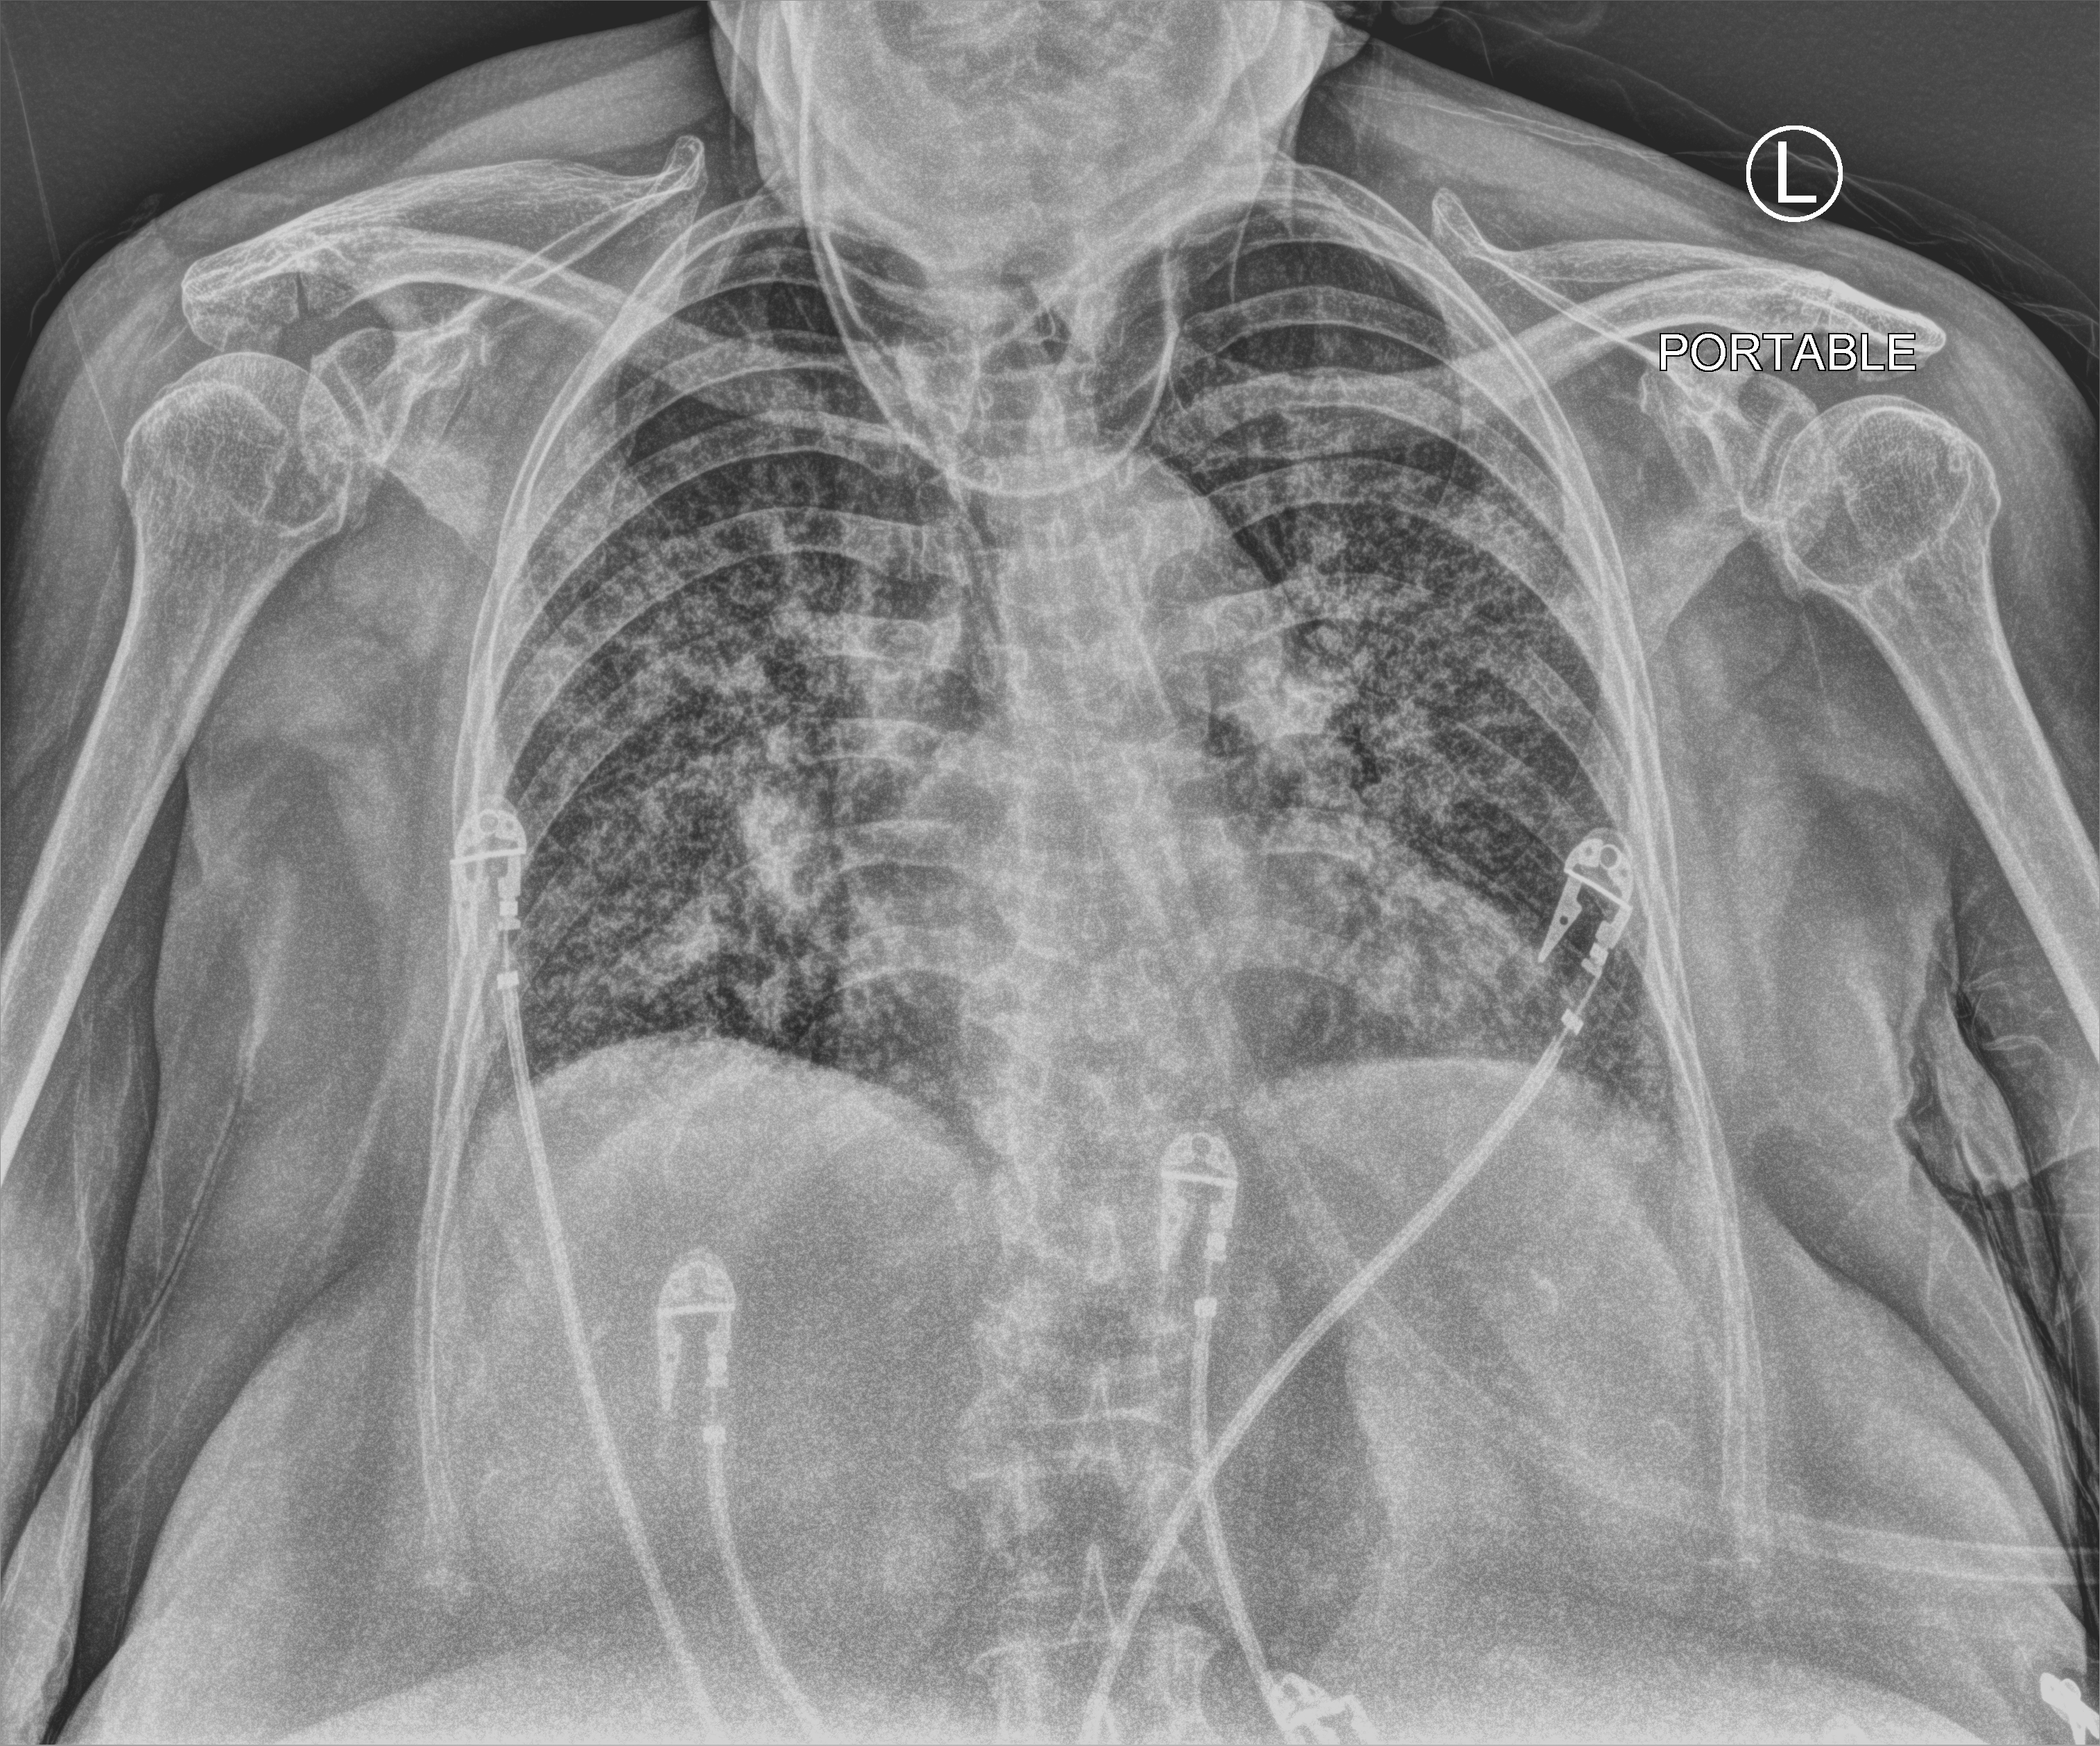
Portable chest radiograph; anteroposterior (AP) projection. Female patient hospitalised with COVID-19, age 75–90 years.
Hospital-stay facts (about this admission, not read from this image; timing relative to this image not recorded):
- mechanically ventilated during this hospital stay: no